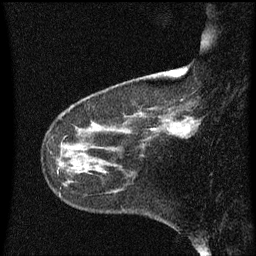
Breast MRI (dynamic contrast-enhanced), one sagittal slice; dynamic contrast-enhanced series, image 2 of 3 at this slice position (ordered by acquisition); 1.5 T; TE 4.2 ms, TR 8.4 ms; 2 mm slice thickness; 256 × 256 image matrix. Patient: female, 41 years. From the clinical record (not read from this slice): setting: breast cancer imaged before/during neoadjuvant chemotherapy; receptor status: triple-negative.
Structures marked on this image (semi-automatic segmentation, software-assisted and operator-edited):
- analysis volume of interest (the breast-tissue region the enhancement analysis was run in; not a lesion): bounding box [x1, y1, x2, y2] px = [158, 100, 202, 139]
- tumour enhancement mask (voxels above the 70 % enhancement threshold inside the analysis volume of interest): [187, 120, 194, 131]